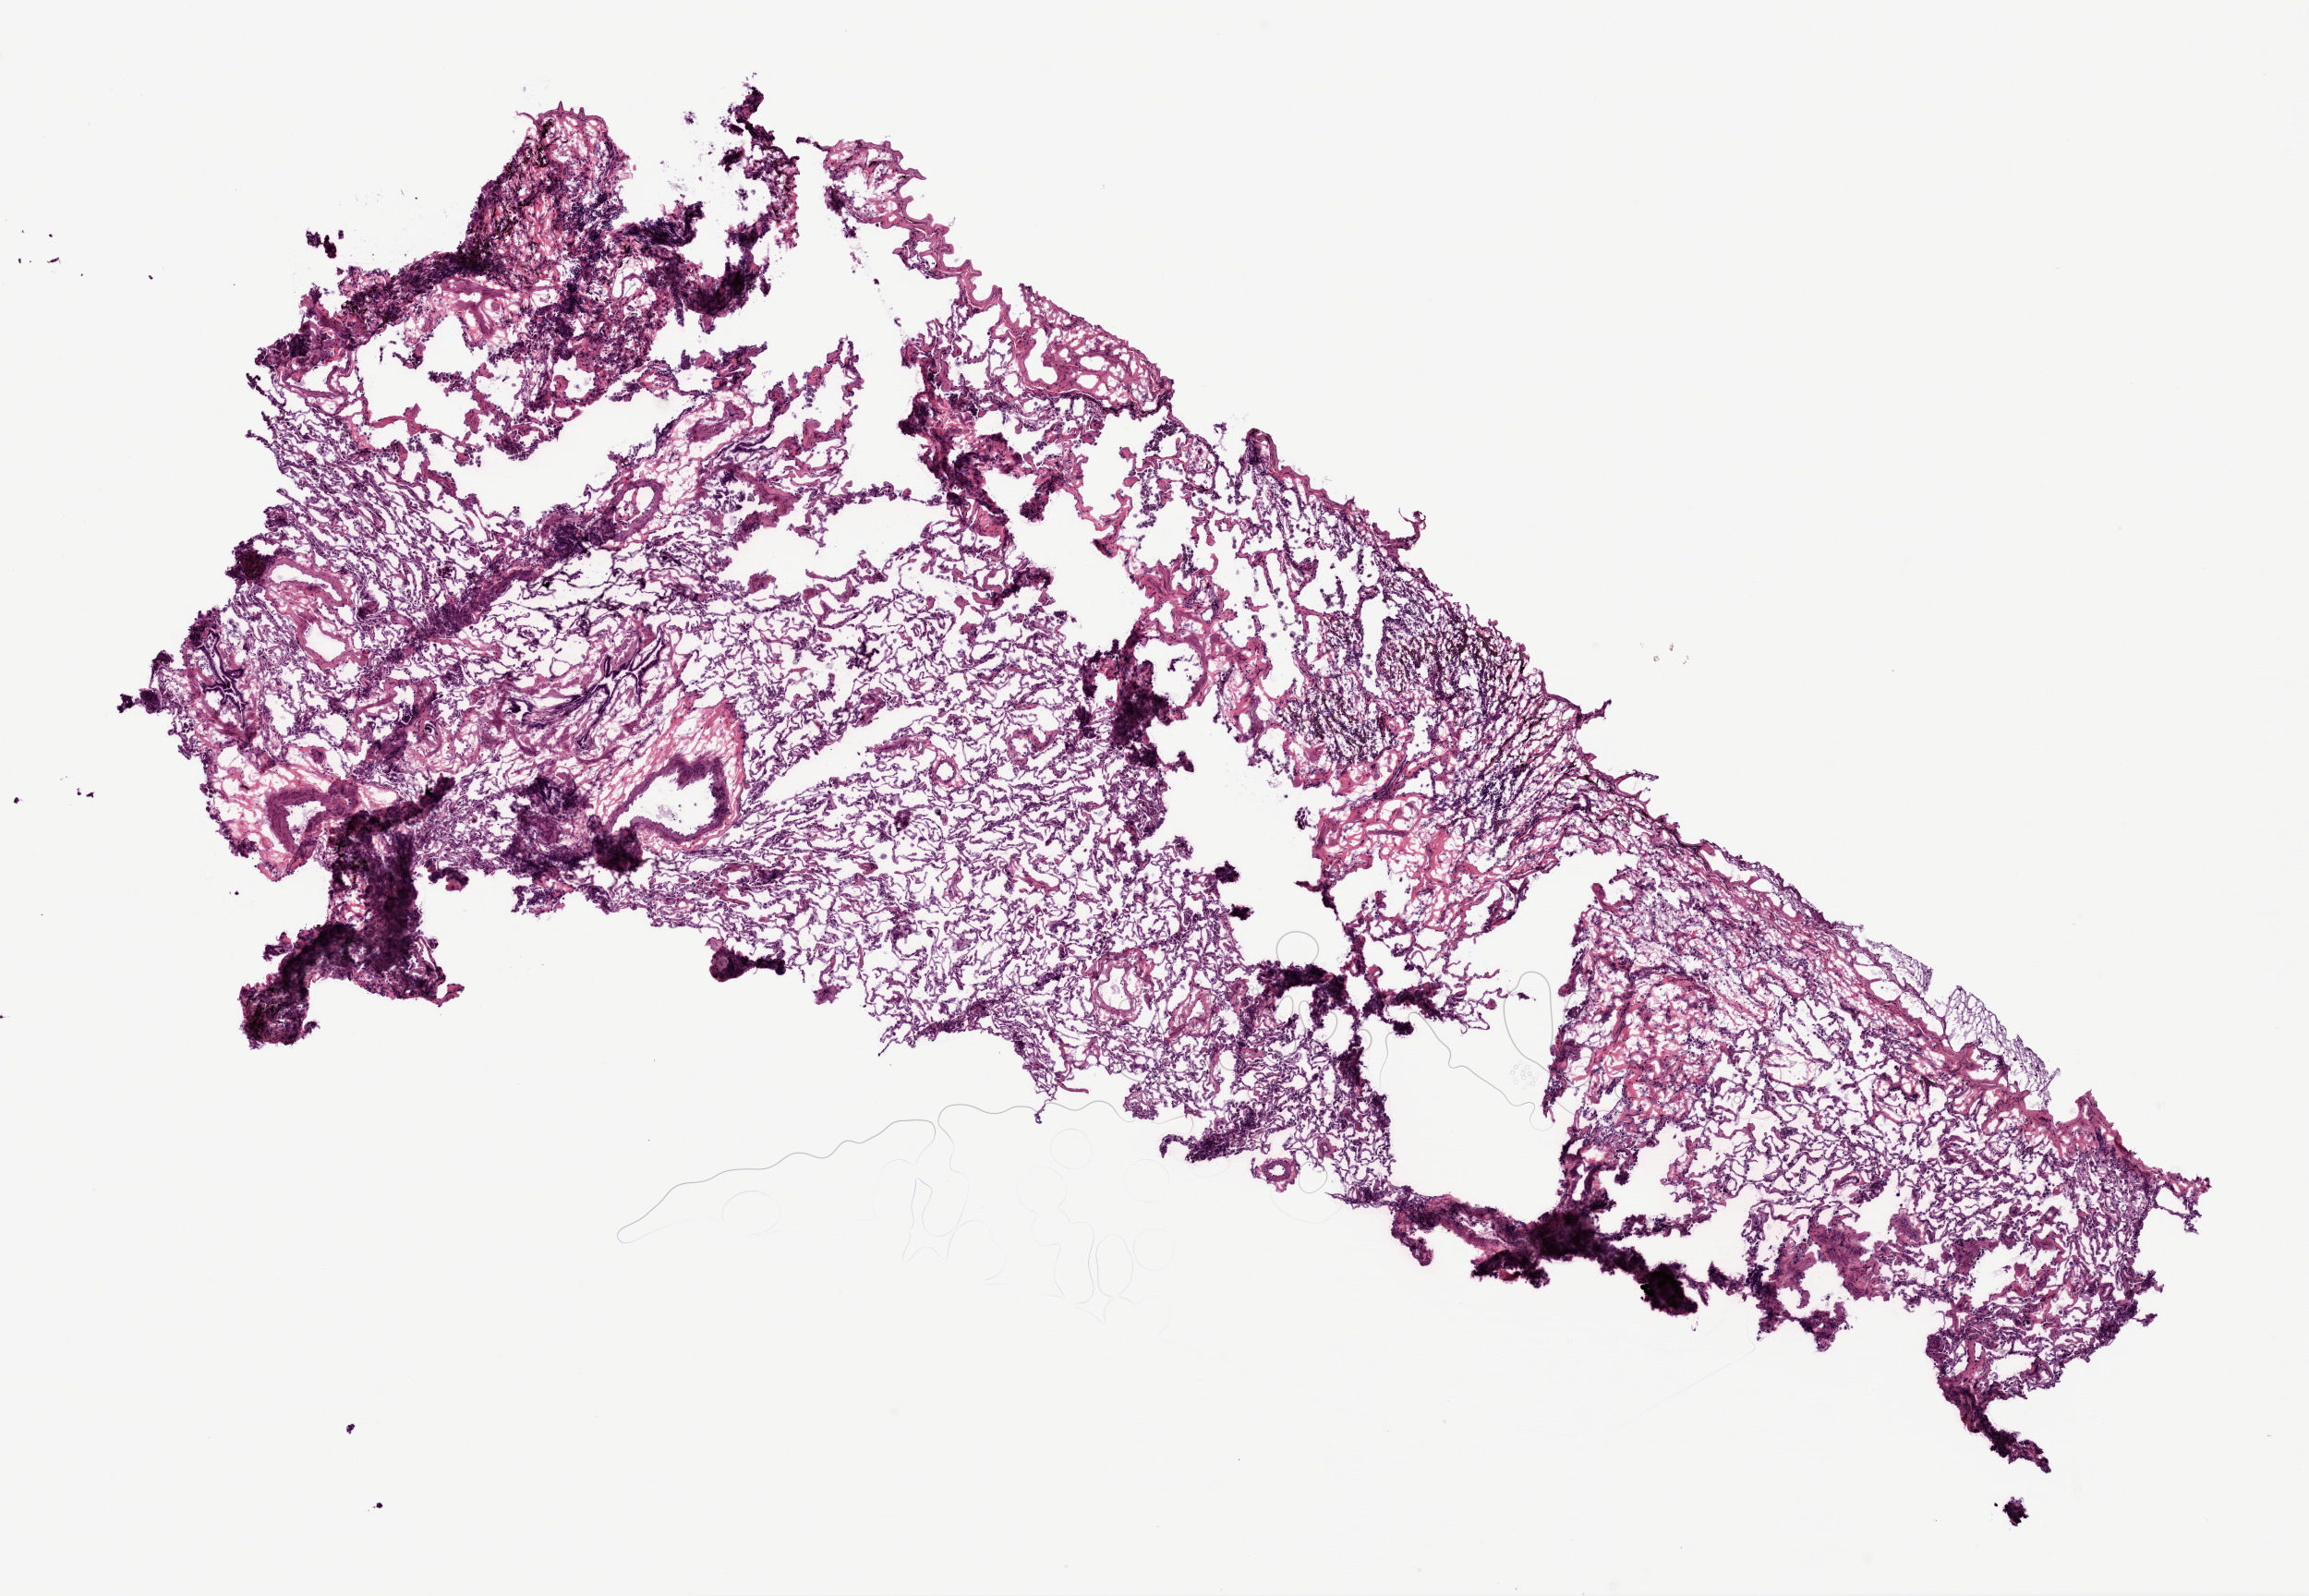
H&E whole-slide image — a low-resolution overview of the entire scanned area, about 10.0 x 6.9 mm (acquisition: 20x scan). Frozen section from the top of the tissue portion. Solid tissue normal (non-tumour tissue) sample from the lung. Male patient; age at initial diagnosis 73 years.
This section: solid tissue normal (non-tumour) sample from the same patient. Patient diagnosis: Squamous cell carcinoma, NOS (upper lobe, lung).